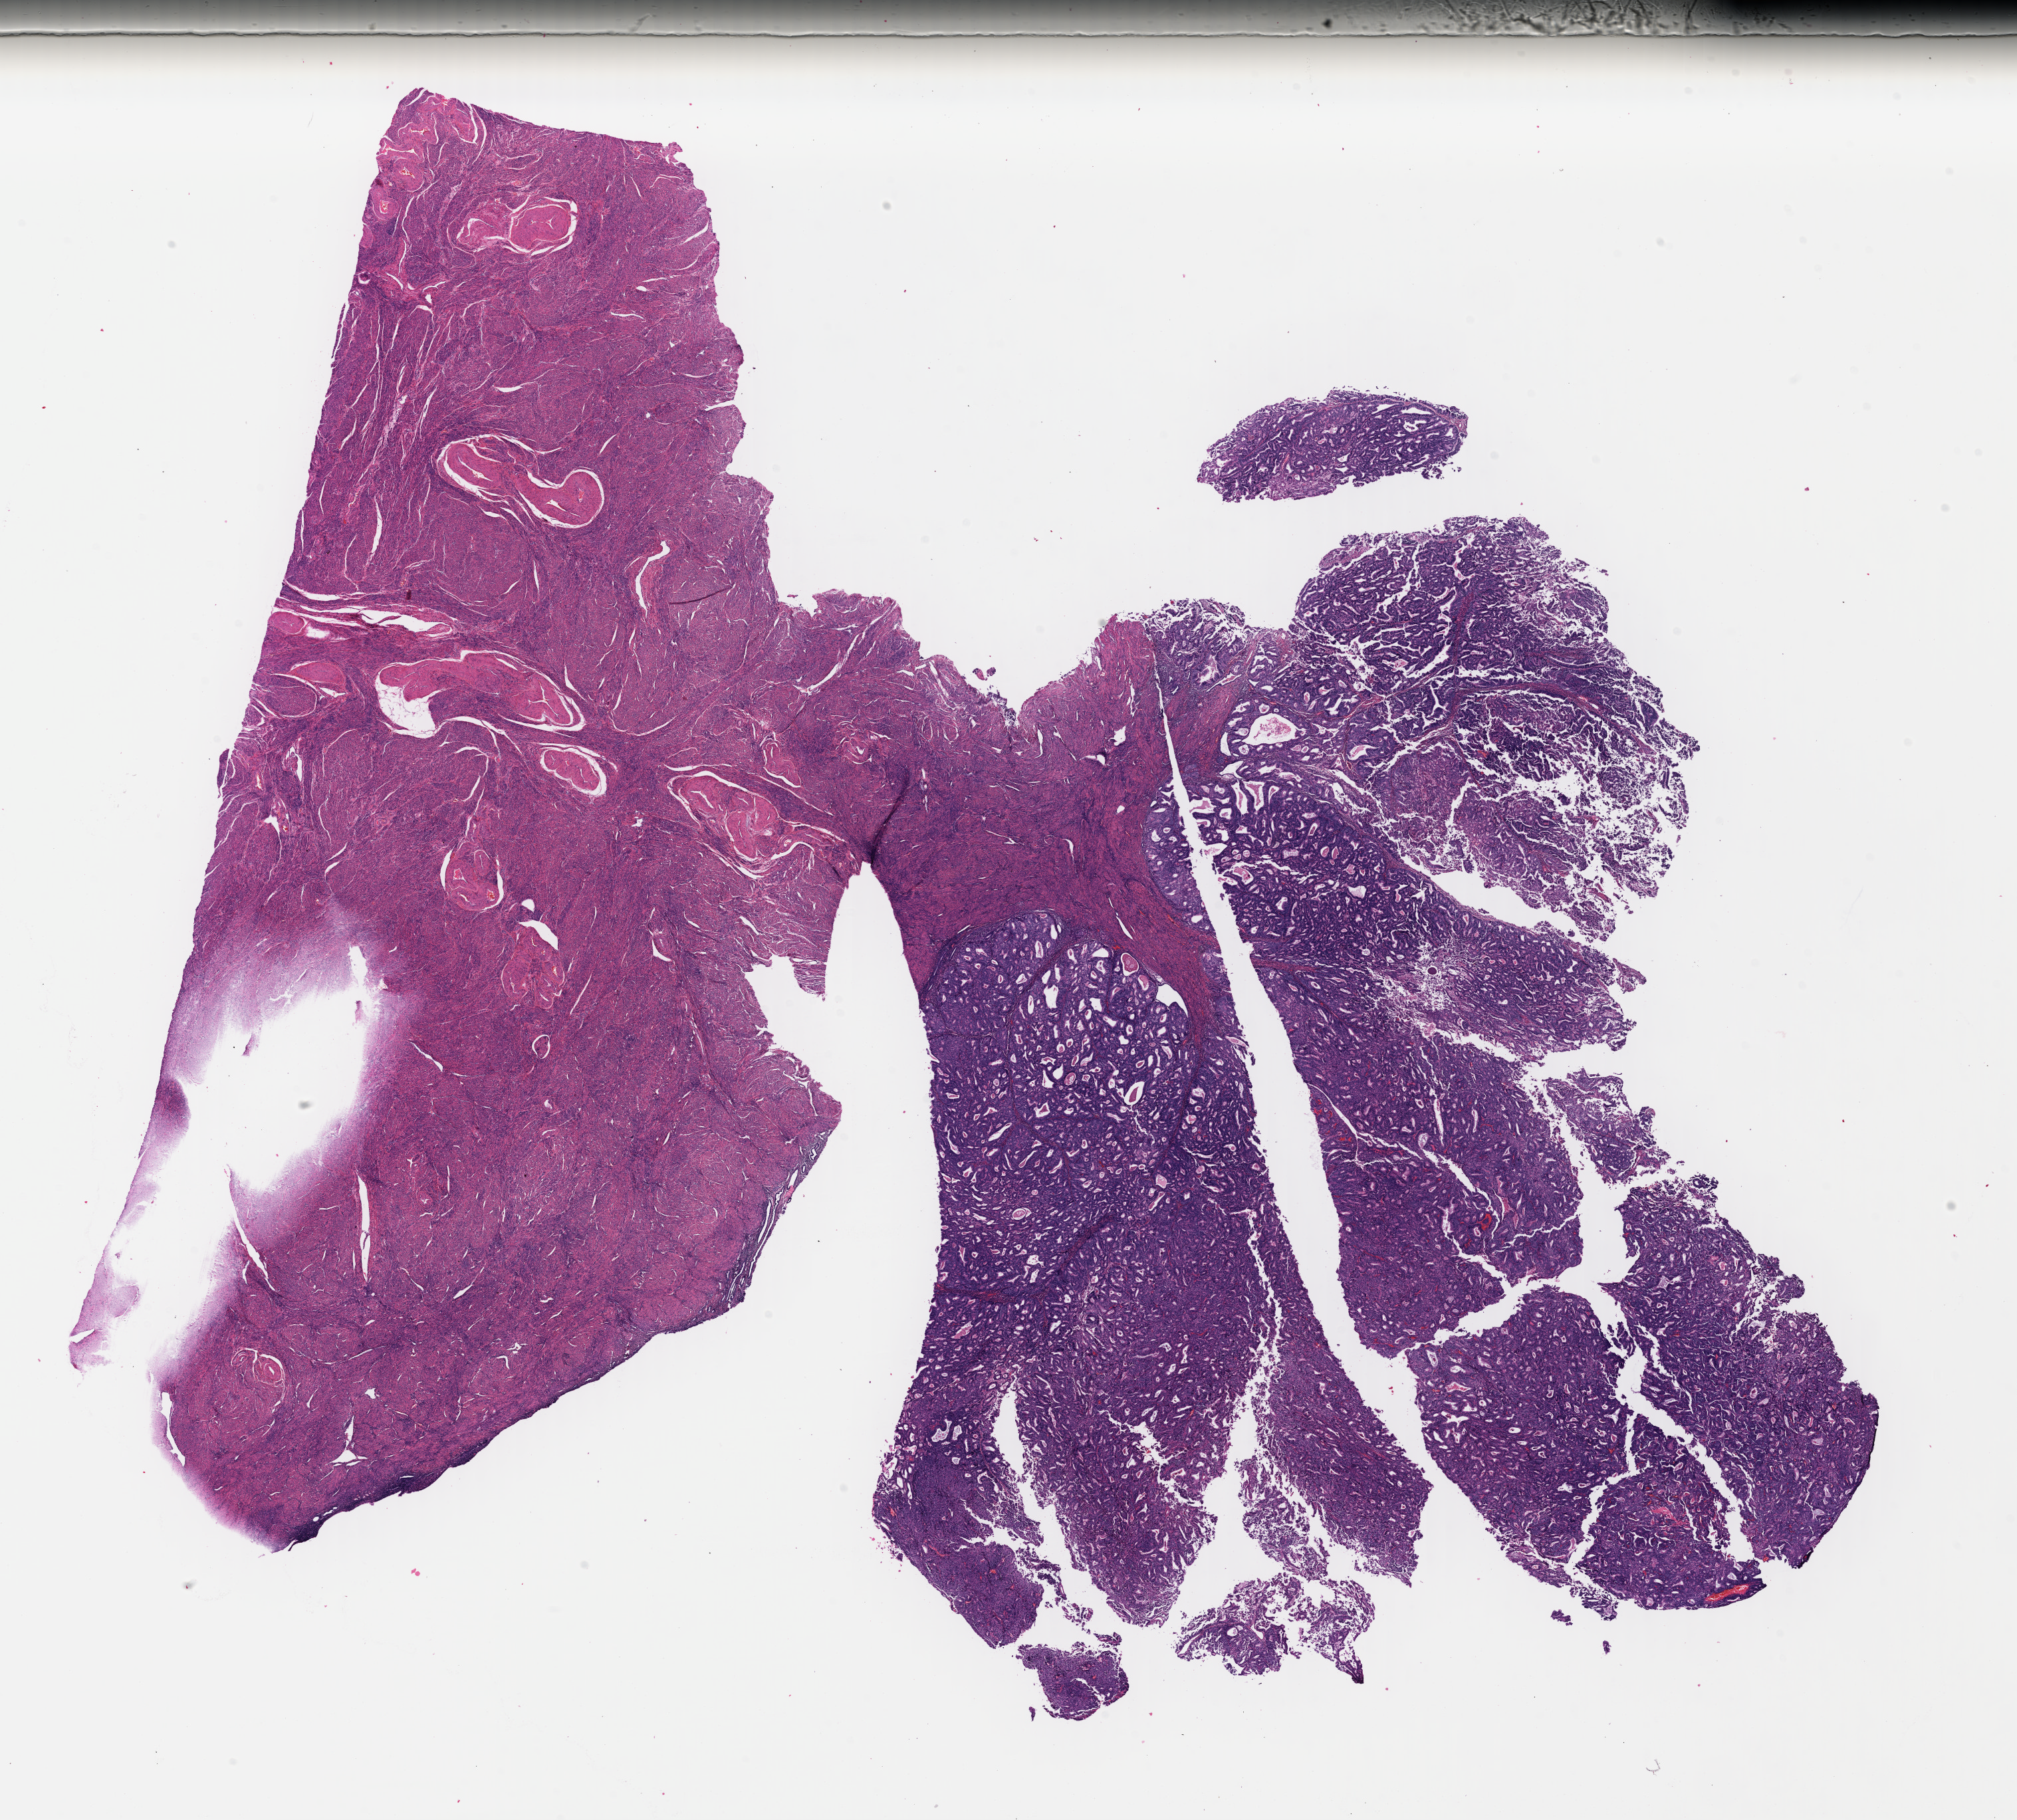
Whole-slide histology image, Hematoxylin and eosin (H&E) stained, shown as a low-resolution overview of the whole scanned area (about 23.8 x 21.5 mm); formalin-fixed paraffin-embedded (FFPE) diagnostic section; uterus, primary tumour sample. Female patient; age at initial diagnosis 57 years. Histologic grade: G2 (moderately differentiated).
FIGO stage: IB. Histologic diagnosis: Endometrioid adenocarcinoma, NOS.